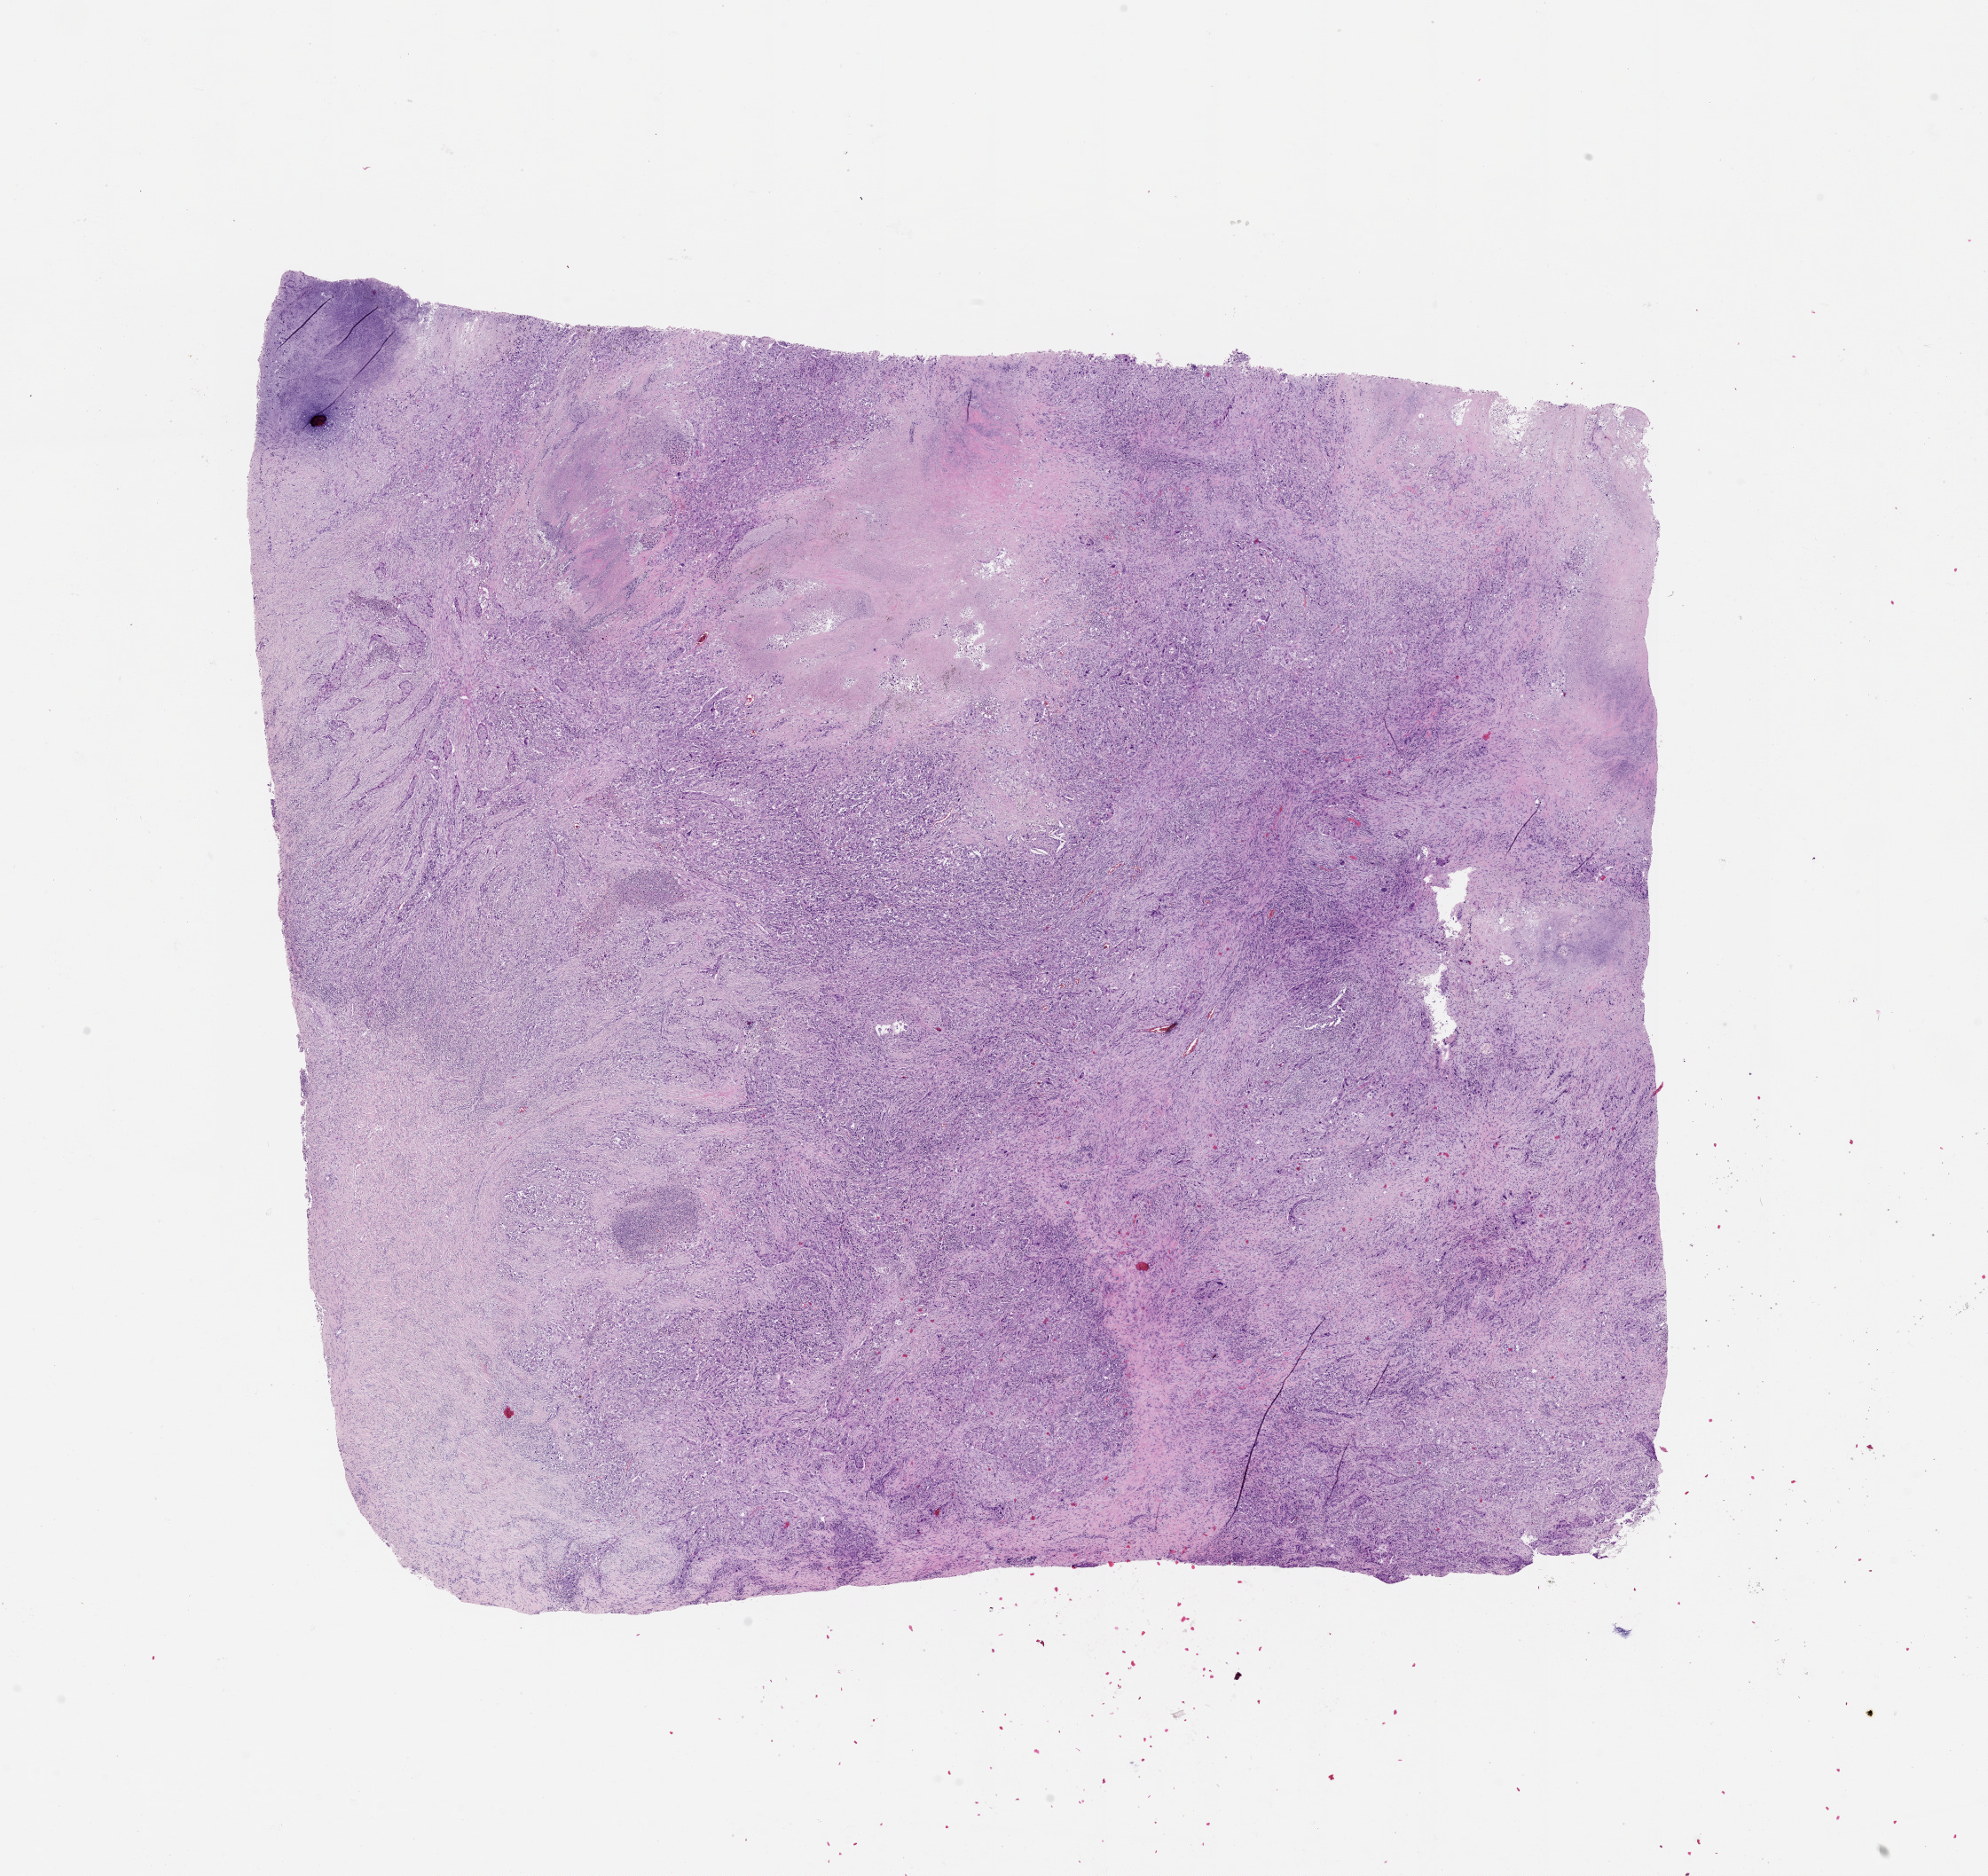
Whole-slide histology image, H&E, shown as a low-resolution overview of the whole scanned area (about 18.0 x 17.0 mm, acquisition: 20x scan); lung, tissue type not recorded.
* patient diagnosis (cohort enrolment): squamous cell carcinoma (lung)